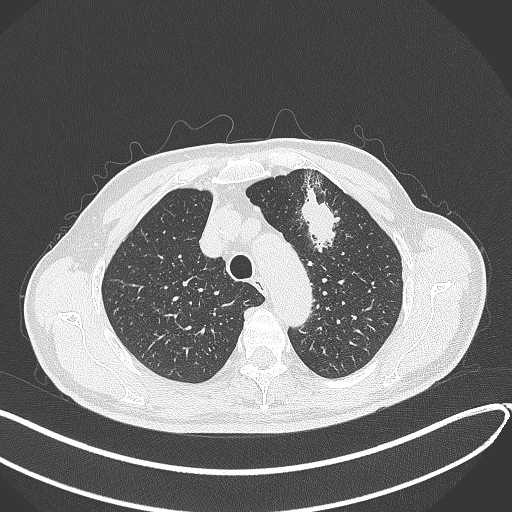
Chest CT, one axial slice; slice 328 of 459 in the series (ordered by position); lung window (W 1500 / L -600 HU); 512 × 512 image matrix. Male patient, age 74 years. Case-level facts recorded for this patient, not image findings: clinical TNM (as recorded): T2b N0 M1c.
Annotated regions visible in this slice (rectangle marked by the reading radiologist):
- lung tumour (recorded histology: adenocarcinoma): bounding box [x1, y1, x2, y2] px = [298, 183, 347, 255]